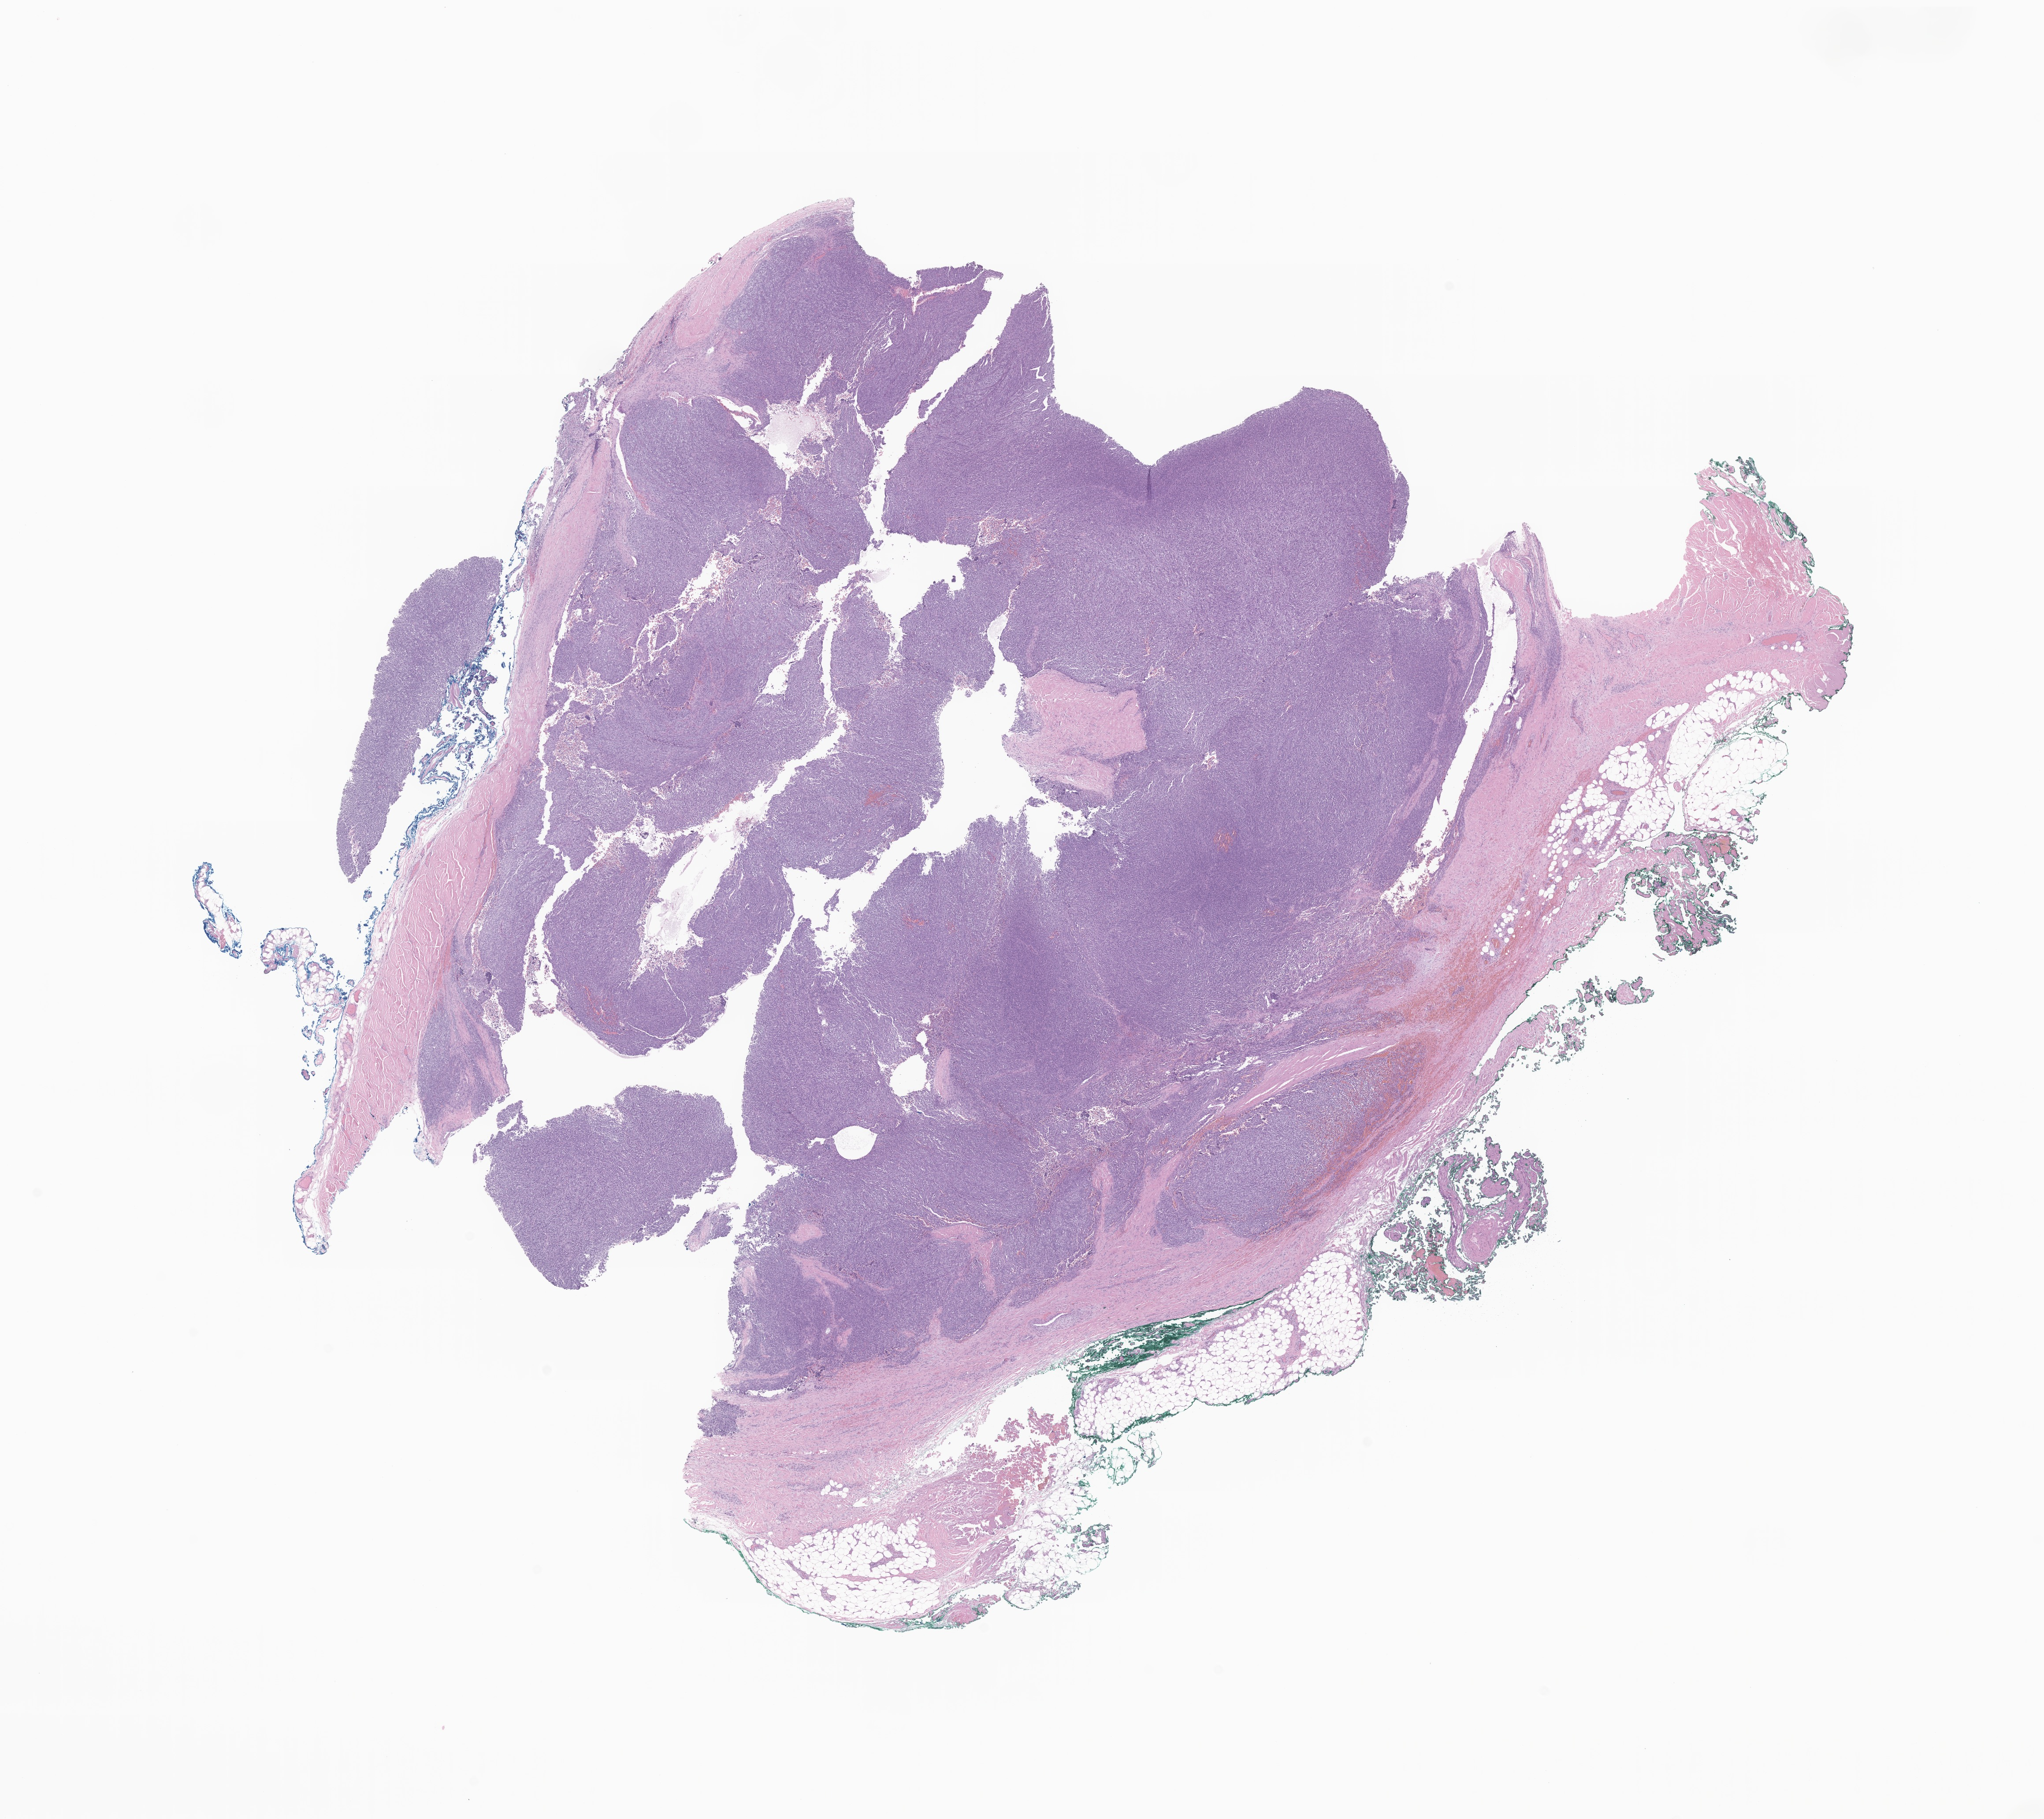
Whole-slide image, haematoxylin and eosin stain of tumor tissue from the lower limb, a low-resolution overview of the entire scanned area, about 19.6 x 17.4 mm; formalin-fixed, paraffin-embedded (FFPE) tissue. Patient: female, age 192 months (16 years).
Diagnosis (ICD-O-3 morphology term): Synovial sarcoma, NOS.